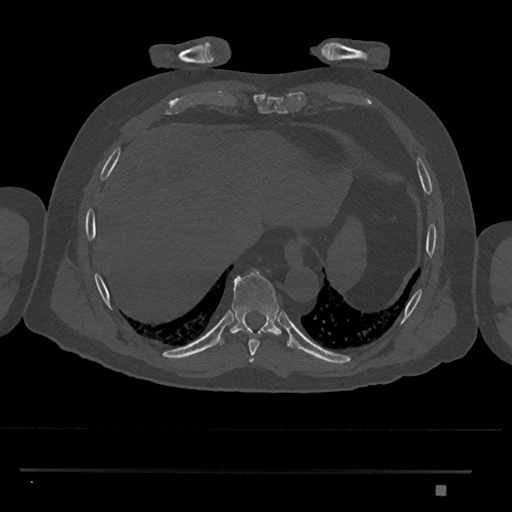
CT including the spine, one axial slice; position 1076 of 1134 along the scan axis; bone window (W 1800 / L 400 HU); 512 × 512 image matrix, field of view 429 × 429 mm. Patient: male, 65 years. From the clinical record (not read from this slice): primary cancer: prostate.
Annotated regions visible in this slice (semi-automatic segmentation, software-assisted and operator-edited):
- T8 vertebra: box from (x=248, y=339) to (x=260, y=362) px
- T9 vertebra: (x=216, y=270)–(x=292, y=348)